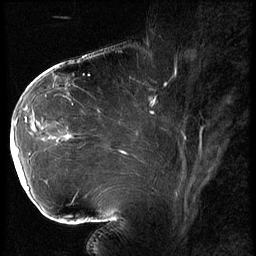
Breast MRI (dynamic contrast-enhanced), one sagittal slice; position 39 of 62 along the scan axis; 3 images stored at this slice position (order not interpretable as contrast timing); 1.5 T; TE 4.2 ms, TR 9 ms; 256 × 256 image matrix, field of view 180 × 180 mm. Patient: female, 43 years. Case-level facts recorded for this patient, not image findings: setting: breast cancer imaged before/during neoadjuvant chemotherapy; receptor status: HER2-positive.
Outlined on this slice (semi-automatically segmented with operator editing):
- analysis volume of interest (the breast-tissue region the enhancement analysis was run in; not a lesion): bounding box [x1, y1, x2, y2] px = [11, 90, 82, 203]
- tumour enhancement mask (voxels above the 140 % enhancement threshold inside the analysis volume of interest): [12, 108, 70, 189]